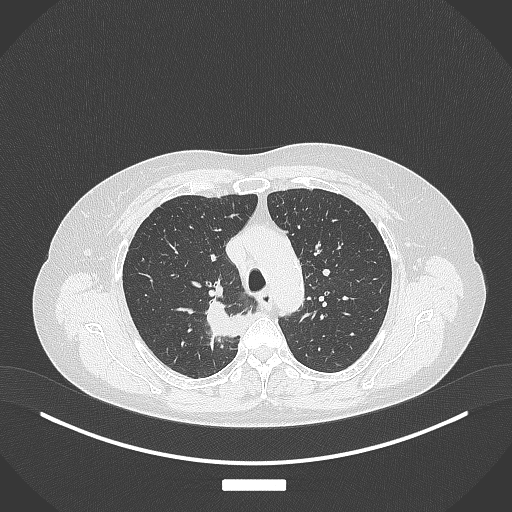
Chest CT, one axial slice; position 283 of 357 along the scan axis; reconstruction kernel B70f; lung window (W 1500 / L -600 HU); 512 × 512 image matrix, field of view 400 × 400 mm. Patient: female, 62 years. Case-level facts recorded for this patient, not image findings: clinical TNM (as recorded): T1c N1 M0.
Structures marked on this image (rectangle marked by the reading radiologist):
- lung tumour (recorded histology: squamous cell carcinoma): bounding box [x1, y1, x2, y2] px = [210, 290, 248, 344]